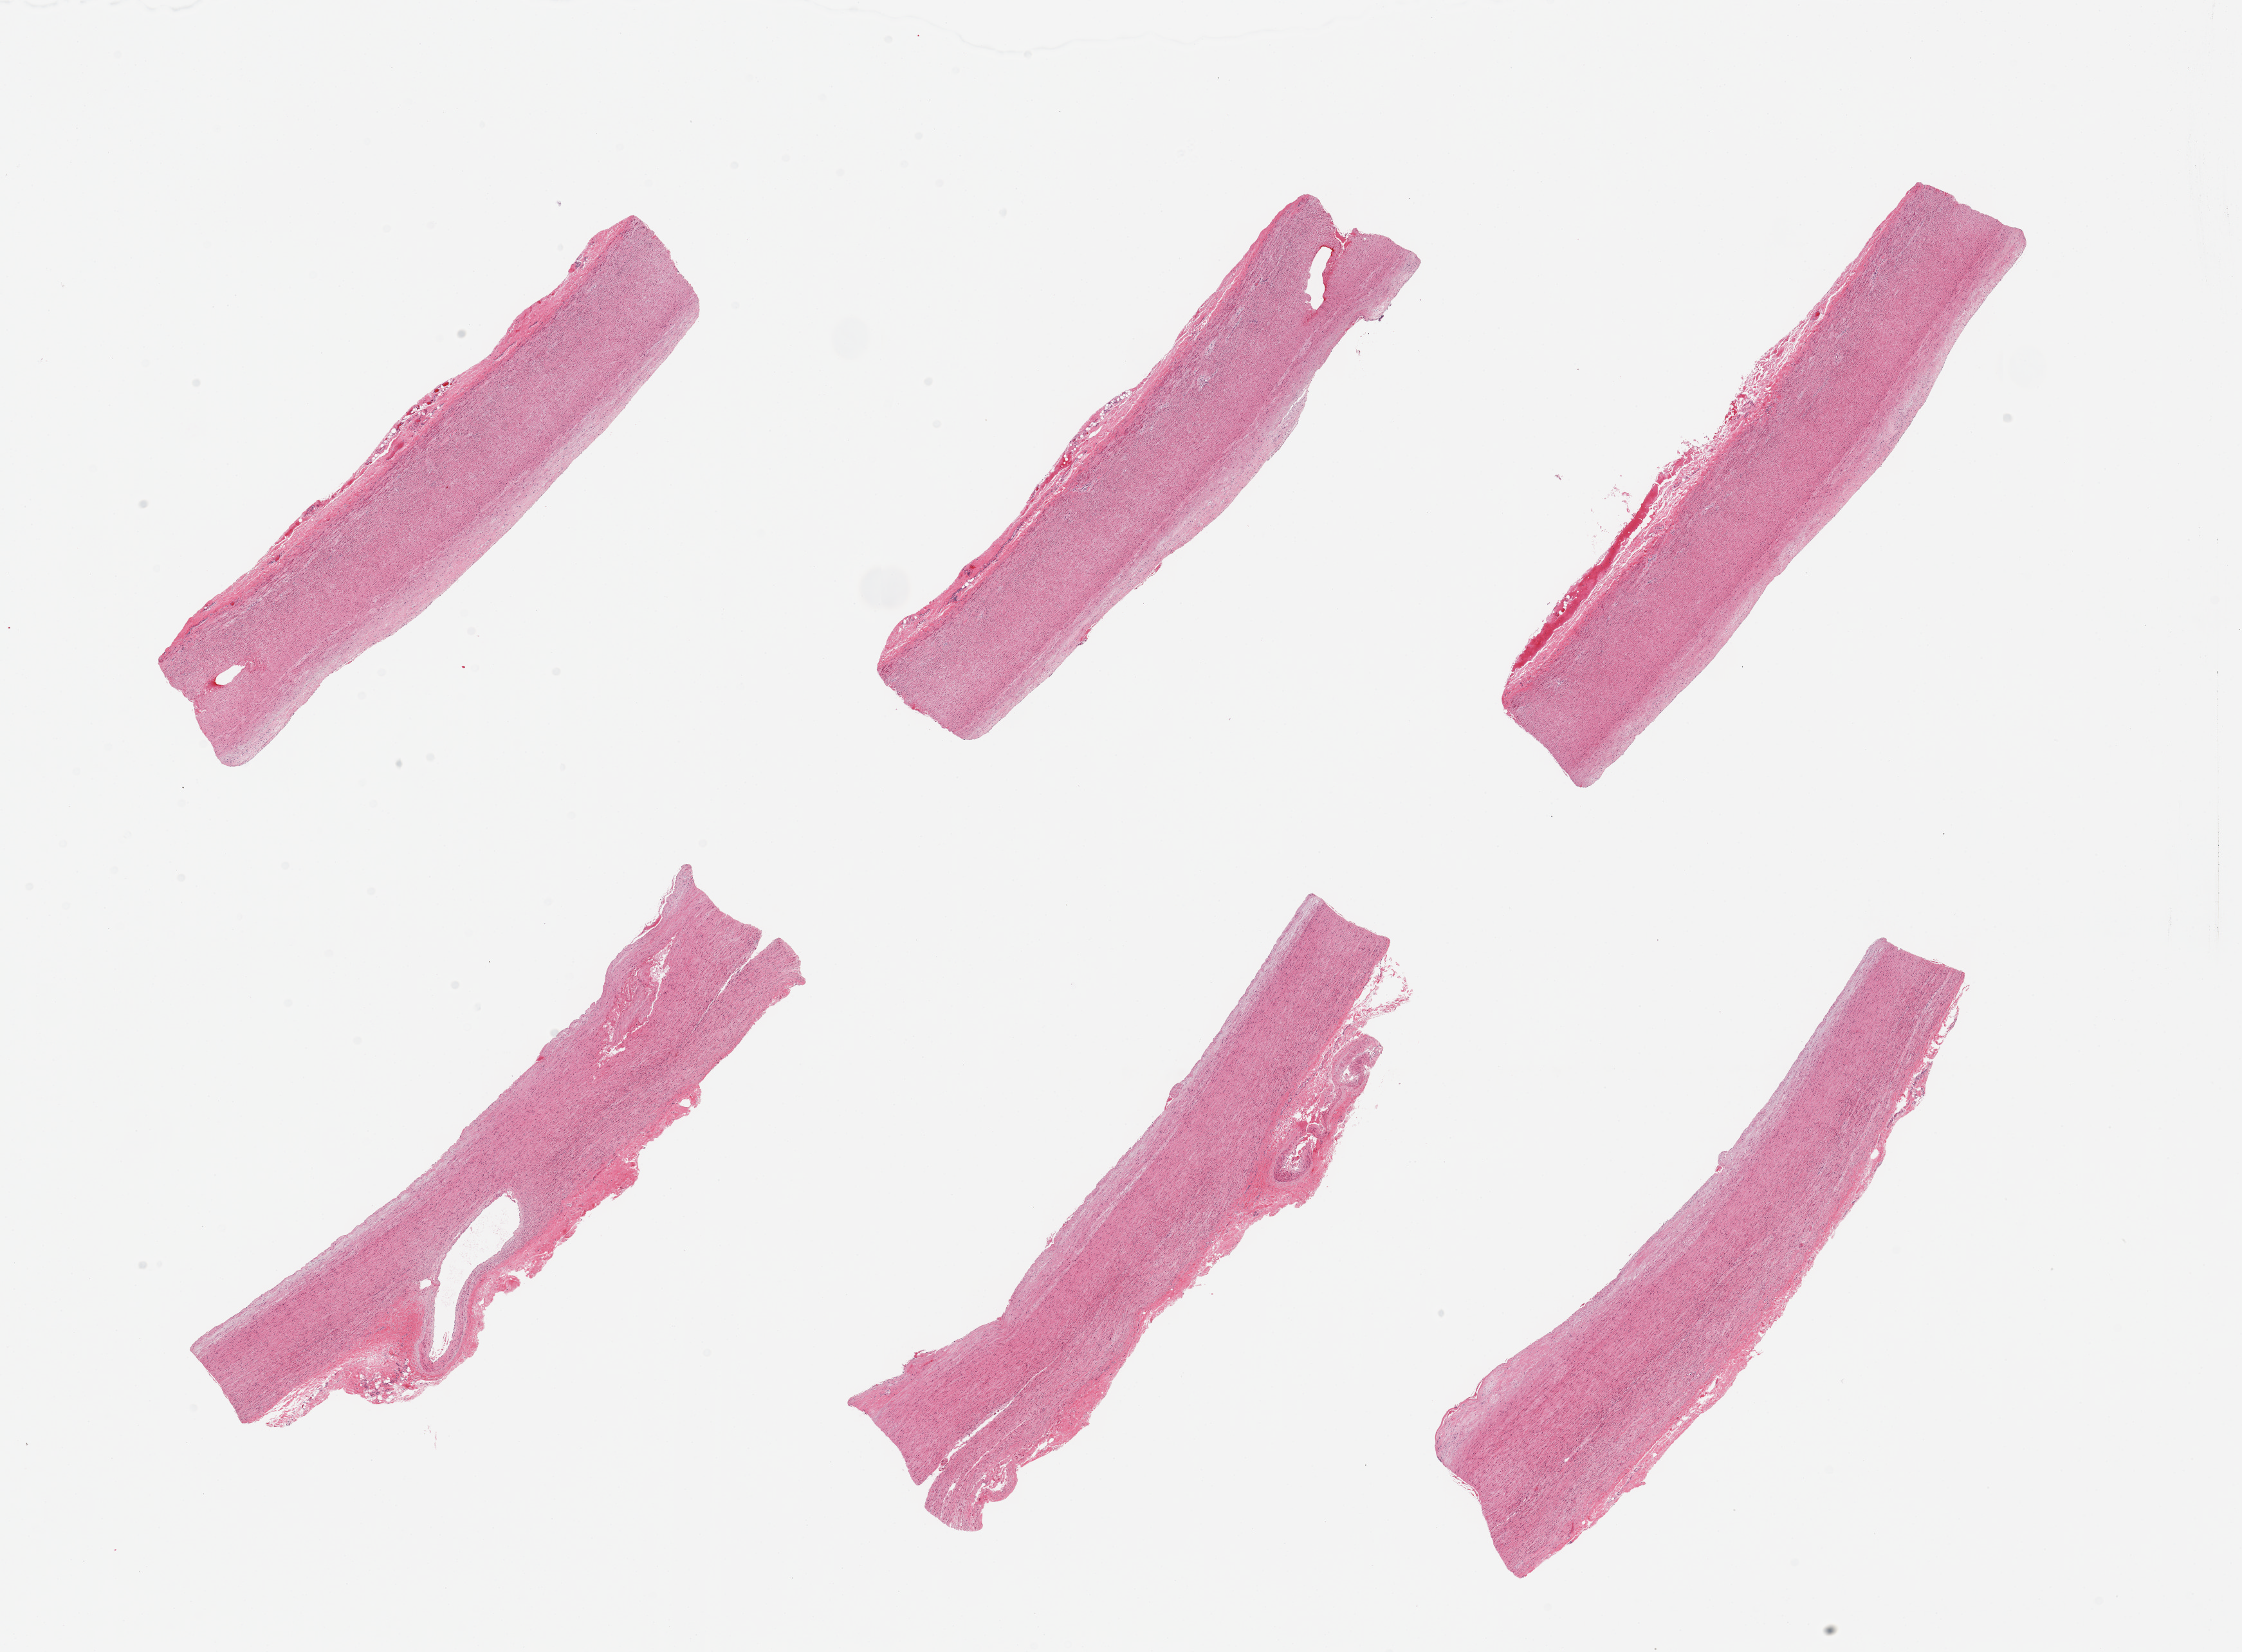
Whole-slide image, H&E stain, shown as a low-resolution overview of the whole scanned area (about 27.6 x 20.3 mm). PAXgene-fixed, paraffin-embedded tissue. Section of aorta (target tissue). Tissue donor sample. Male donor.
Pathologist's review note for this sample: 6 pieces; linear plaques; tributary in 2 pieces.